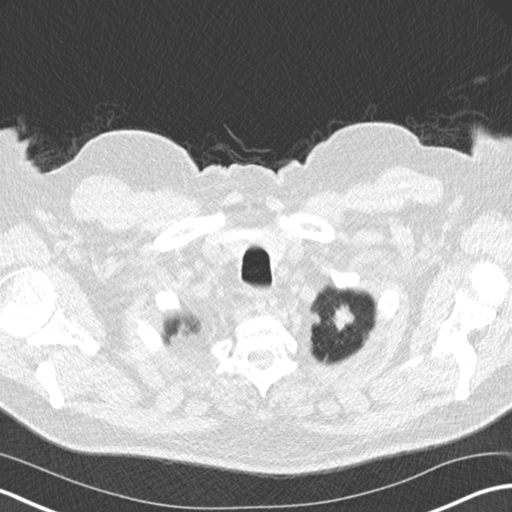
Low-dose screening chest CT, one axial slice; slice 157 of 175 in the series (ordered by position); reconstruction kernel B30f; 120 kVp; lung window (W 1500 / L -600 HU); 2 mm slice thickness; 512 × 512 image matrix, field of view 351 × 351 mm.
Outlined on this slice (manually delineated by an expert):
- lesion 1 (tumor, upper lobe of left lung): bounding box (x1, y1, x2, y2) in pixels: (334, 306, 354, 330)